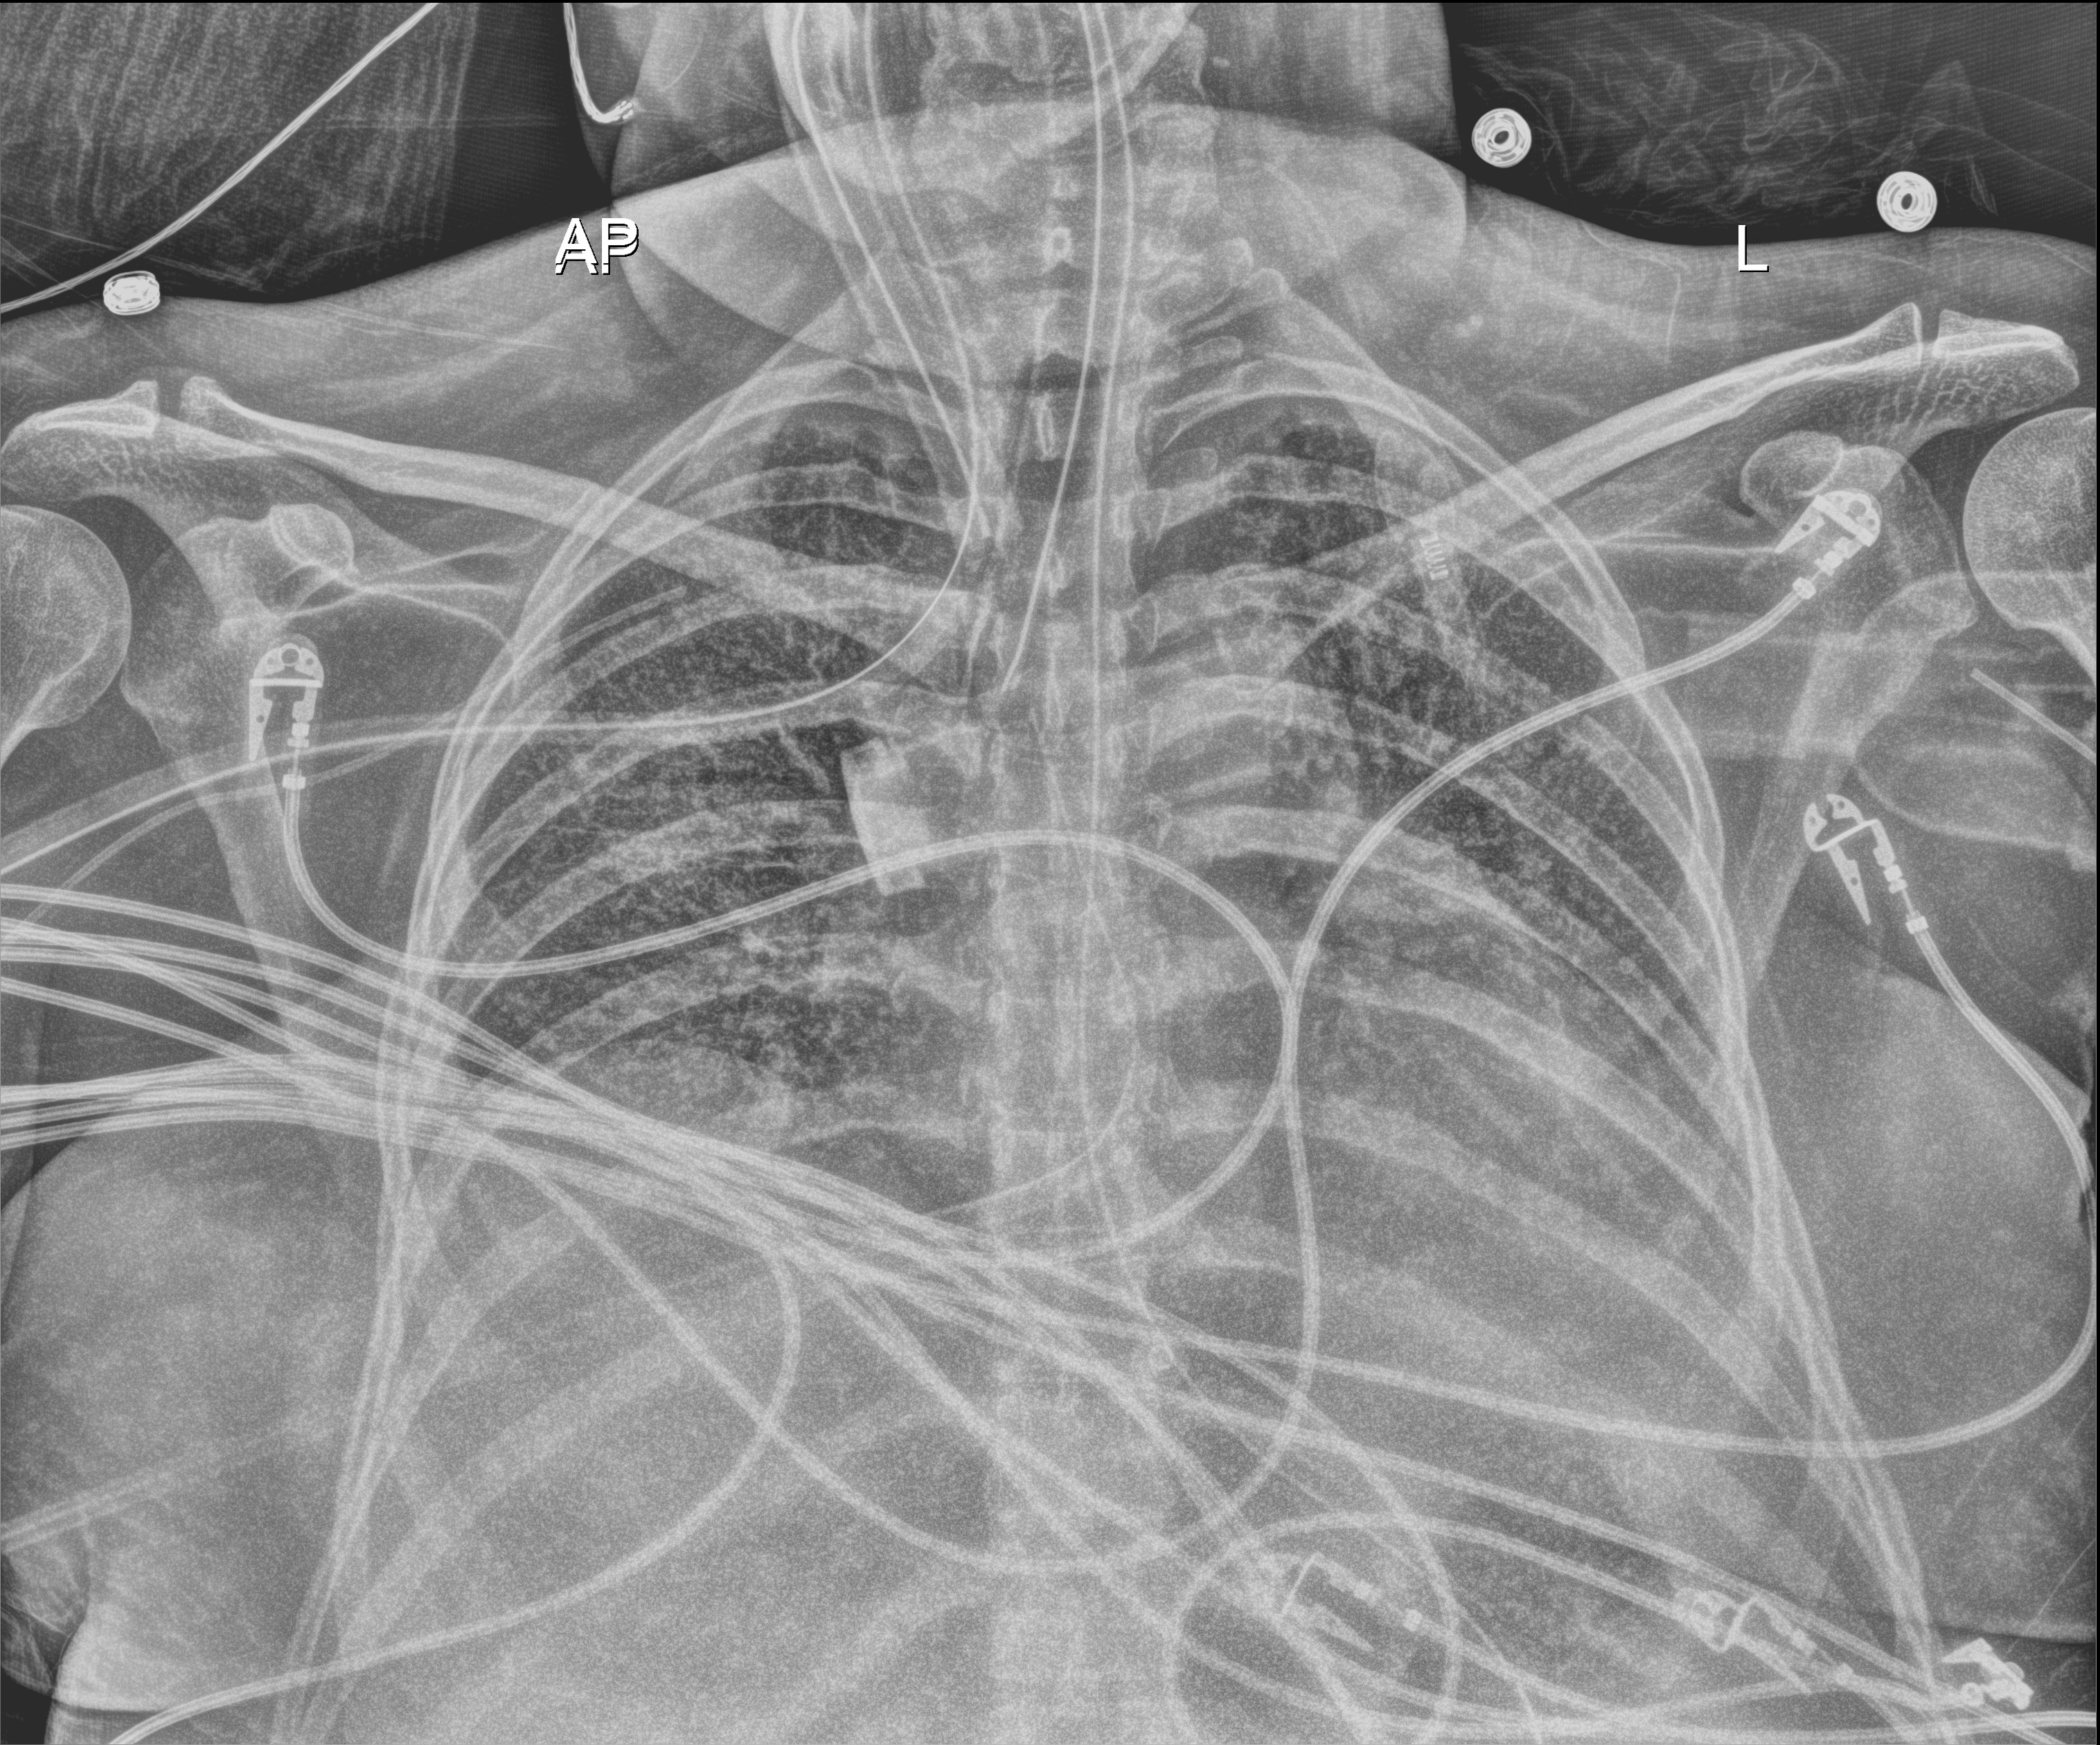
Portable chest radiograph; anteroposterior (AP) projection. Patient hospitalised with COVID-19; female, aged 18–59 years.
Admission-level facts for this patient (not findings on this image; timing relative to this image not recorded):
- mechanically ventilated during this hospital stay: yes
- other chronic lung disease (admission record): yes